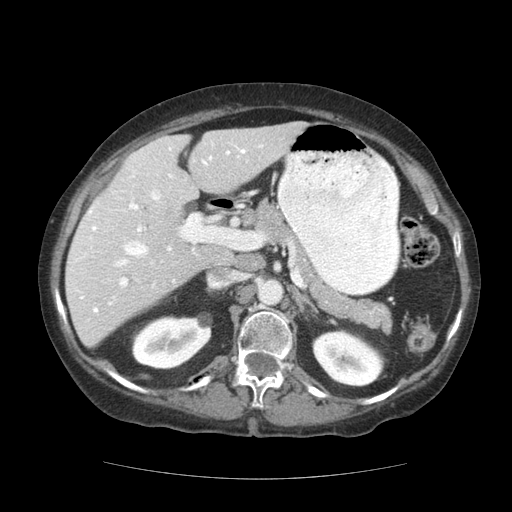
Contrast-enhanced abdominal CT (liver protocol), one axial slice. Position 71 of 111 along the scan axis. Reconstruction kernel STANDARD. 140 kVp. Soft-tissue window (W 400 / L 40 HU). 2.5 mm slice thickness. 512 × 512 image matrix. Case-level facts recorded for this patient, not image findings: diagnosis: hepatocellular carcinoma (patient treated with transarterial chemoembolisation; whether this scan precedes or follows treatment is not stated here); TNM stage (as recorded): Stage-I; Child-Pugh class: A; tumour differentiation: moderately-poorly differentiated; tumour nodularity: uninodular.
Outlined on this slice (semi-automatic segmentation, software-assisted and operator-edited):
- liver parenchyma outside the tumour (the mass and vessels are separate outlines, so this box may not span the whole liver): bounding box <66,122,306,346> (left, top, right, bottom; pixels)
- liver vessels: <74,143,263,312>